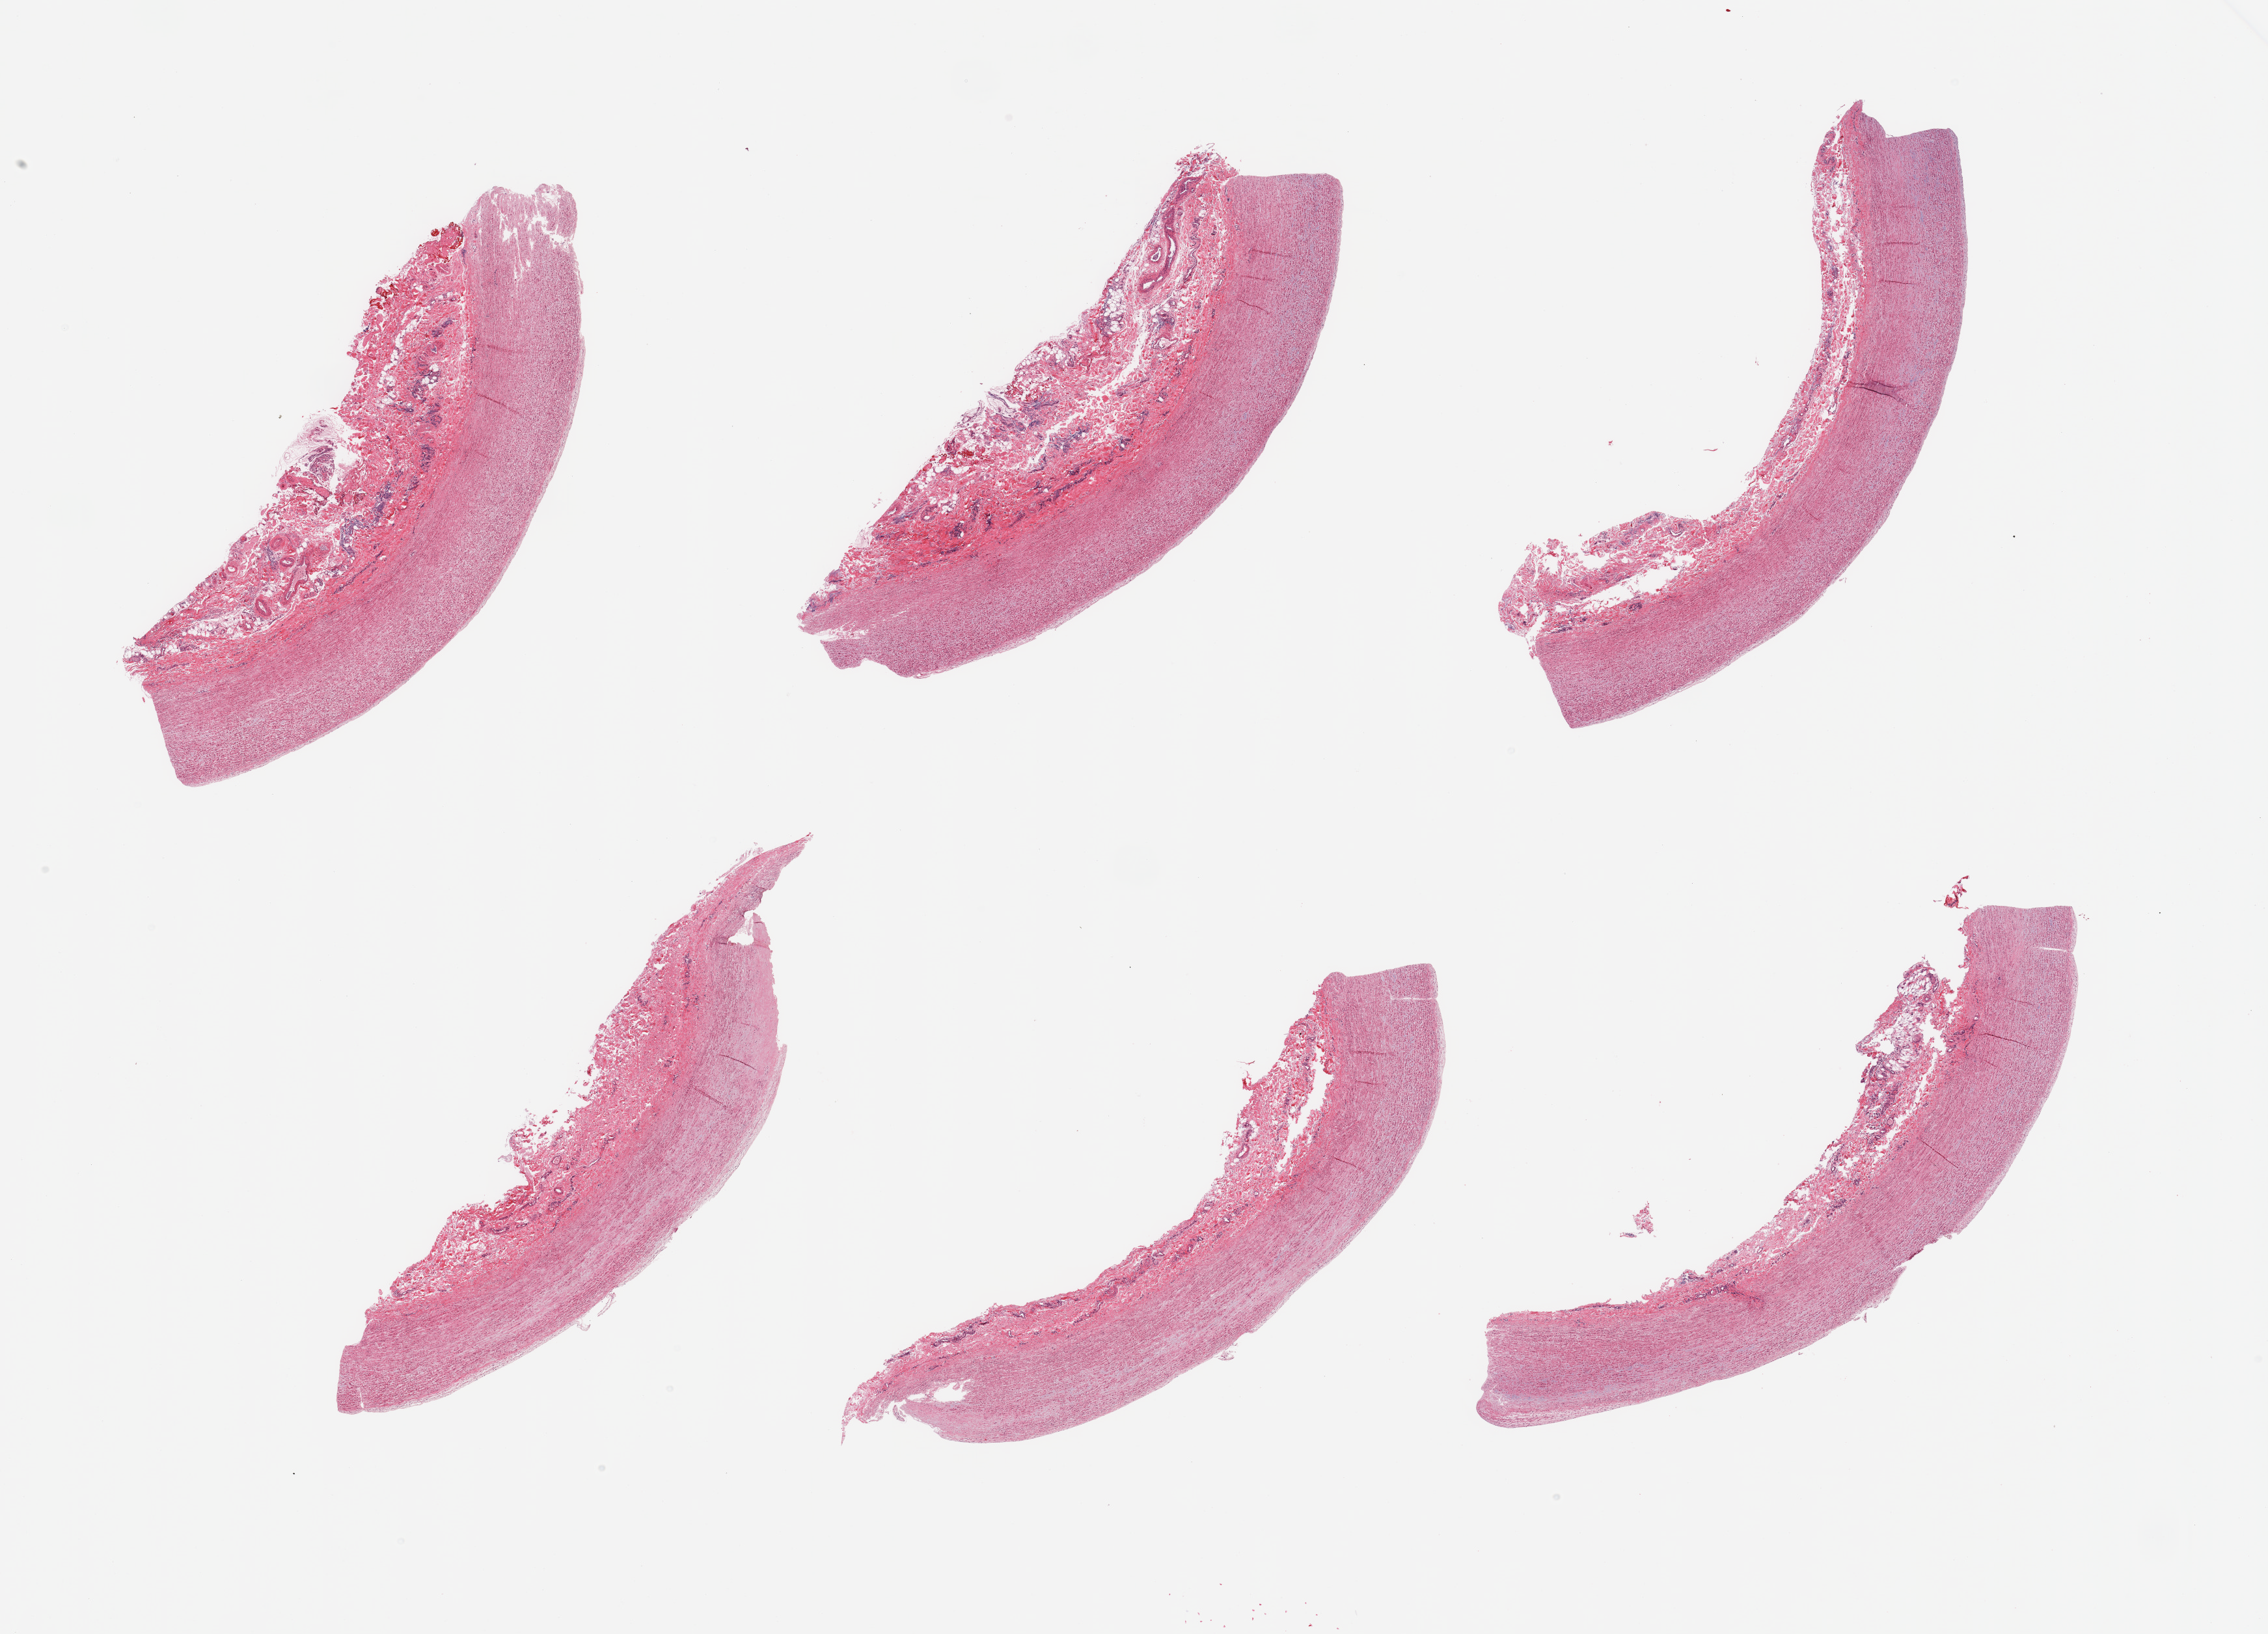
Digitized hematoxylin and eosin (H&E)-stained section, brightfield, whole scanned area (about 27.6 x 19.9 mm, slide scanned at 20x) shown as a low-resolution overview, PAXgene-fixed, paraffin-embedded tissue, sampled site (target tissue): aorta, tissue donor sample. Female donor.
- pathologist's review note for this sample: 6 pieces, adherent serosa/fascia up to ~1.5mm